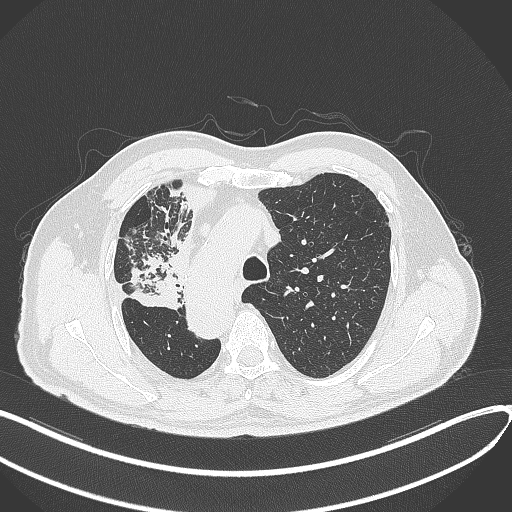
Chest CT, one axial slice; slice 236 of 300 in the series (ordered by position); 120 kVp; lung window (W 1500 / L -600 HU); 512 × 512 image matrix, field of view 400 × 400 mm. Patient: male, 67 years. From the clinical record (not read from this slice): clinical TNM (as recorded): T2a N0 M0.
Outlined on this slice (rectangle marked by the reading radiologist):
- lung tumour (recorded histology: squamous cell carcinoma): bounding box (x1, y1, x2, y2) in pixels: (127, 247, 183, 313)